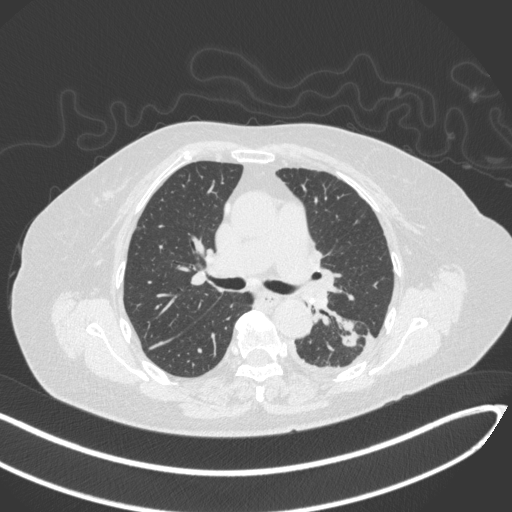
Chest CT, one axial slice. Position 193 of 270 along the scan axis. Lung window (W 1500 / L -600 HU). 512 × 512 image matrix, field of view 400 × 400 mm. Patient: female, 76 years. From the clinical record (not read from this slice): clinical TNM (as recorded): T1c N0 M0.
Outlined on this slice (bounding box drawn by a radiologist):
- lung tumour (recorded histology: adenocarcinoma): bounding box (x1, y1, x2, y2) in pixels: (337, 329, 362, 349)